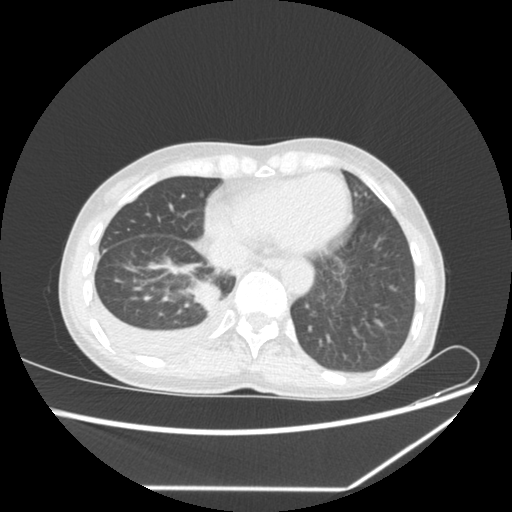
Chest CT, one axial slice; slice 1 of 1 in the series (ordered by position); reconstruction kernel SOFT; 80 kVp; lung window (W 1500 / L -600 HU); 5 mm slice thickness; 512 × 512 image matrix. Patient: female, 59 years. Case-level facts recorded for this patient, not image findings: clinical TNM (as recorded): T1c N1 M1.
Annotated regions visible in this slice (bounding box drawn by a radiologist):
- lung tumour (recorded histology: adenocarcinoma): box from (x=189, y=280) to (x=219, y=311) px